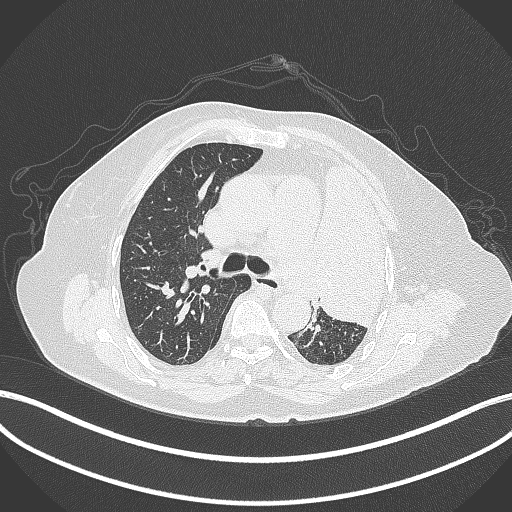
Chest CT, one axial slice. Position 252 of 399 along the scan axis. Reconstruction kernel B70f. 120 kVp. Lung window (W 1500 / L -600 HU). 1 mm slice thickness. 512 × 512 image matrix, field of view 400 × 400 mm. Patient: female, 75 years. Case-level facts recorded for this patient, not image findings: clinical TNM (as recorded): T3 N3 M1.
Annotated regions visible in this slice (rectangle marked by the reading radiologist):
- lung tumour (recorded histology: adenocarcinoma): box from (x=307, y=151) to (x=389, y=332) px